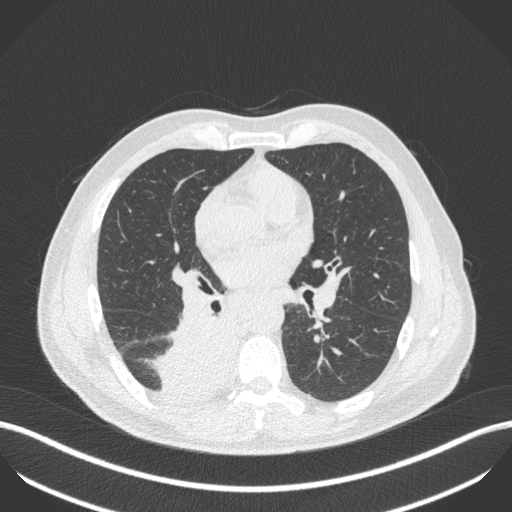
Chest CT, one axial slice; slice 247 of 451 in the series (ordered by position); reconstruction kernel B31f; lung window (W 1500 / L -600 HU); 1 mm slice thickness; 512 × 512 image matrix, field of view 400 × 400 mm. Patient: male, 61 years. Case-level facts recorded for this patient, not image findings: clinical TNM (as recorded): T1 N0 M0; histopathological grade: G3.
Structures marked on this image (bounding box drawn by a radiologist):
- lung tumour (recorded histology: small cell carcinoma): bounding box (x1, y1, x2, y2) in pixels: (138, 312, 241, 408)